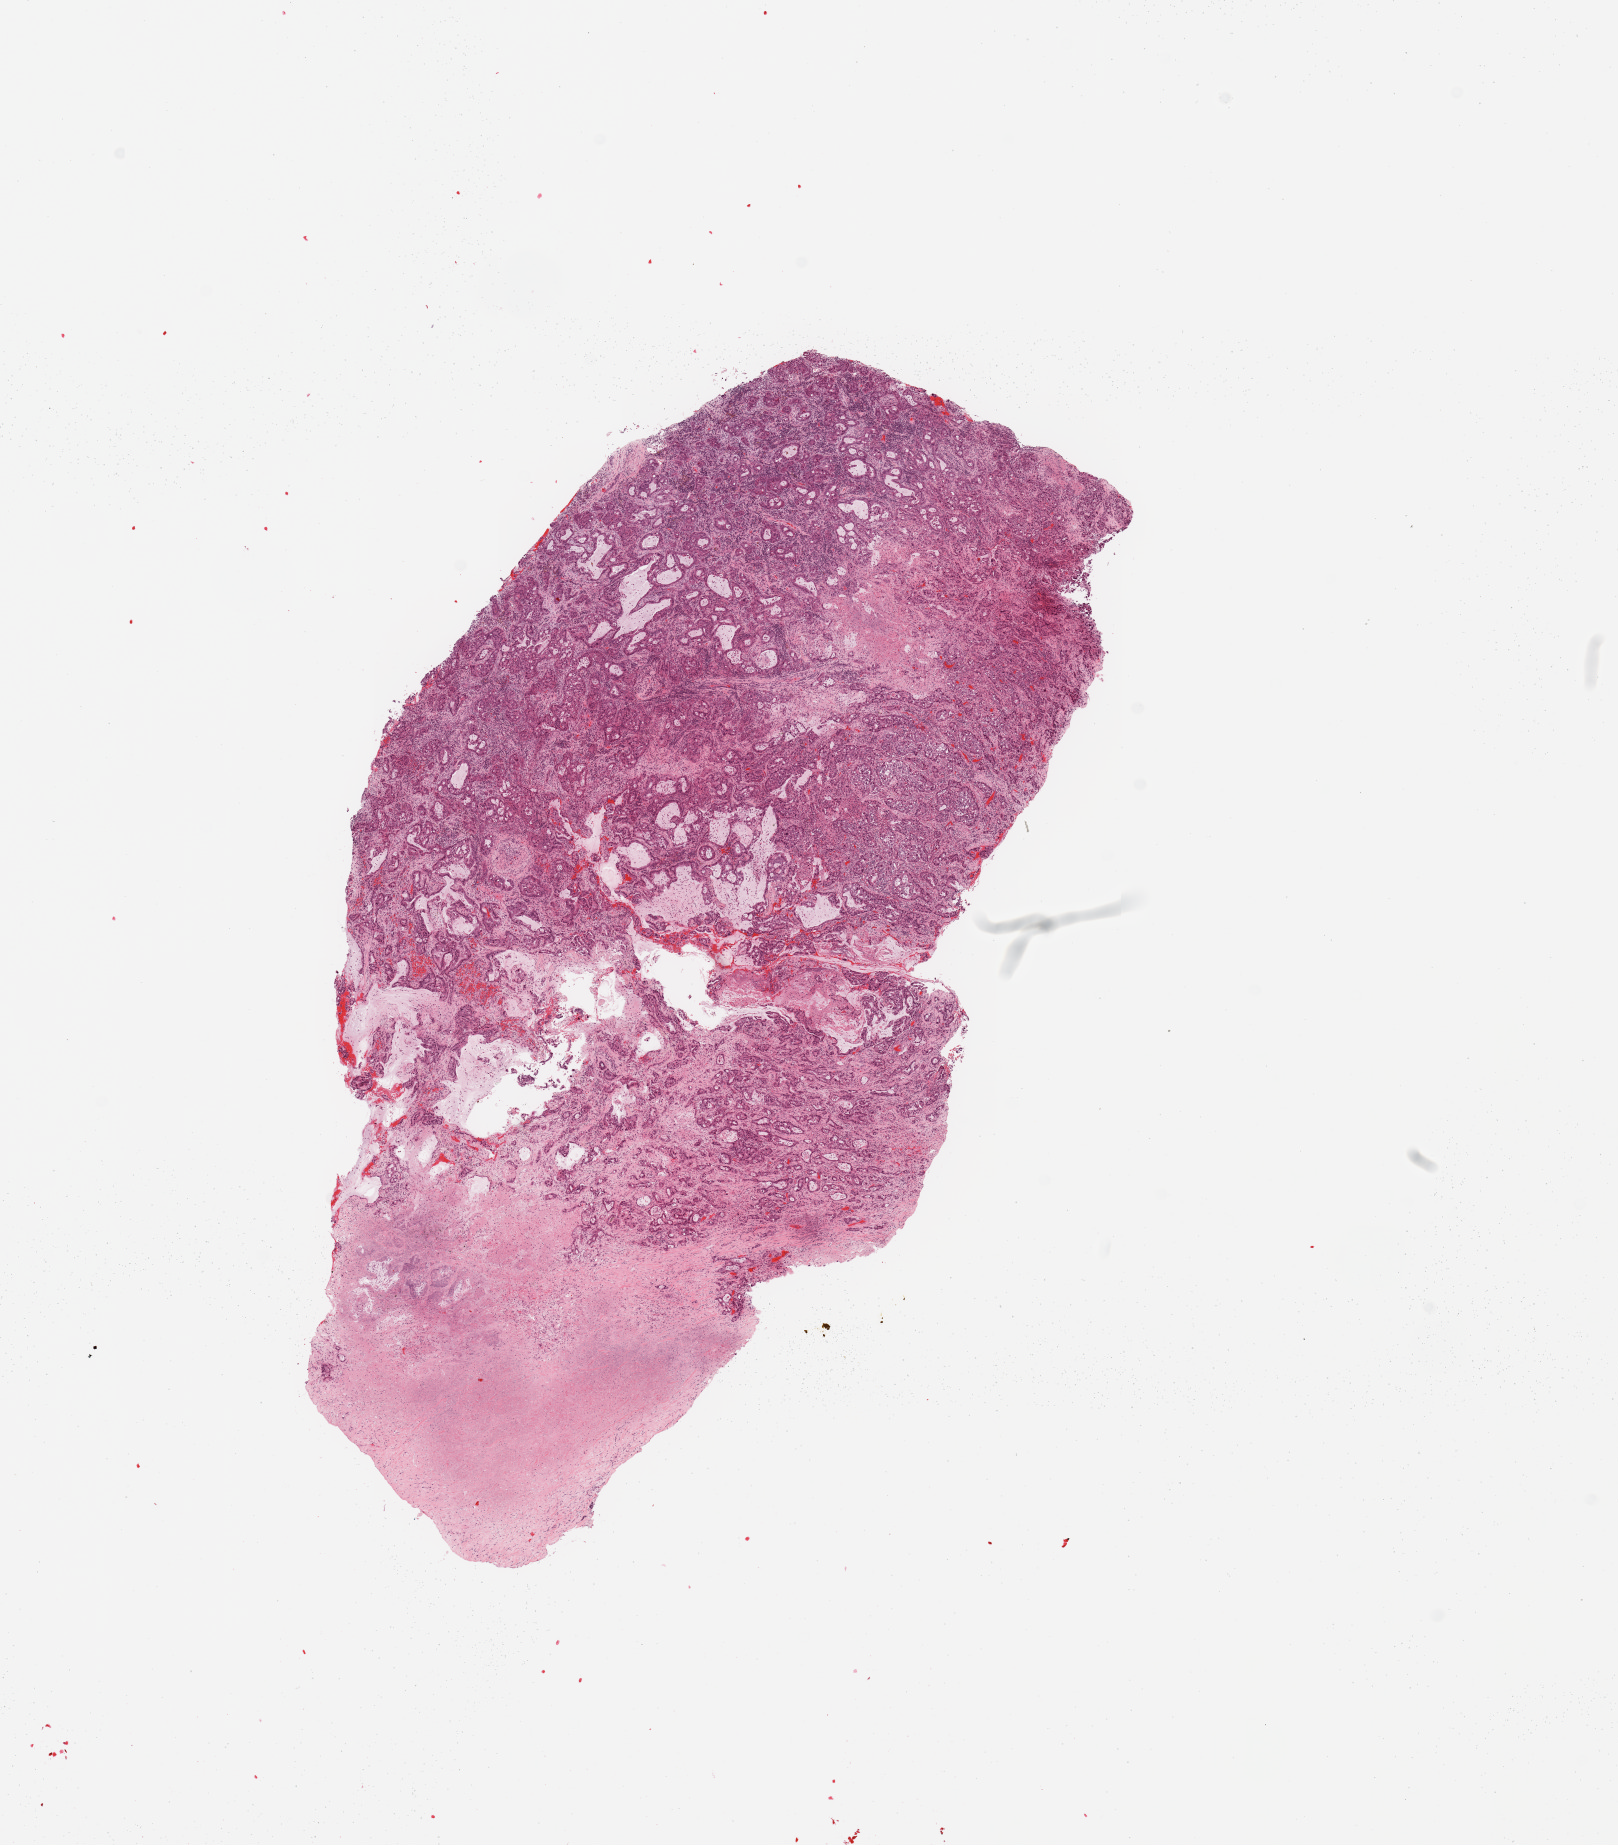
Digitized H&E-stained tissue section (whole slide), whole scanned area (about 12.8 x 14.6 mm, acquisition: 20x scan) shown as a low-resolution overview, lung, tumour tissue. Patient: male, age 66 years.
Histologic diagnosis: Adenocarcinoma, NOS.